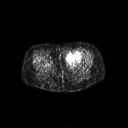
FDG PET of an extremity soft-tissue mass (from a PET/CT study), one axial slice. Slice 27 of 267 in the series (ordered by position). 3.27 mm slice thickness. 128 × 128 image matrix. Female patient, age 47 years. From the clinical record (not read from this slice): histological type: myxofibrosarcoma; grade: intermediate; site of the primary tumour: left thigh.
Outlined on this slice (expert contour drawn on MRI and transferred to this co-registered scan by the dataset authors):
- gross tumour volume including surrounding oedema: bounding box <65,51,82,65> (left, top, right, bottom; pixels)
- gross tumour volume (mass): <65,51,82,64>